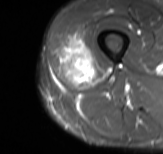
MRI of an extremity soft-tissue mass, one axial slice. Position 24 of 61 along the scan axis. STIR. MR volume resampled by the dataset authors to the PET/CT grid (not the native acquisition matrix). 163 × 154 image matrix. Male patient. From the clinical record (not read from this slice): histological type: poorly differentiated synovial sarcoma; grade: high; site of the primary tumour: right buttock.
Outlined on this slice (expert contour drawn on MRI and transferred to this co-registered scan by the dataset authors):
- gross tumour volume including surrounding oedema: box from (x=57, y=34) to (x=108, y=90) px
- gross tumour volume (mass): (x=59, y=37)–(x=95, y=86)